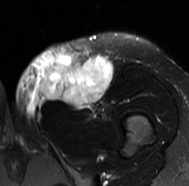
MRI of an extremity soft-tissue mass, one axial slice; slice 31 of 77 in the series (ordered by position); T2-weighted fat-saturated; MR volume resampled by the dataset authors to the PET/CT grid (not the native acquisition matrix); 3.27 mm slice thickness; 189 × 186 image matrix, field of view 185 × 182 mm. Female patient. Case-level facts recorded for this patient, not image findings: histological type: leiomyosarcoma; grade: high; site of the primary tumour: groin.
Annotated regions visible in this slice (expert contour drawn on MRI and transferred to this co-registered scan by the dataset authors):
- gross tumour volume including surrounding oedema: box from (x=15, y=45) to (x=112, y=119) px
- gross tumour volume (mass): (x=38, y=57)–(x=112, y=108)